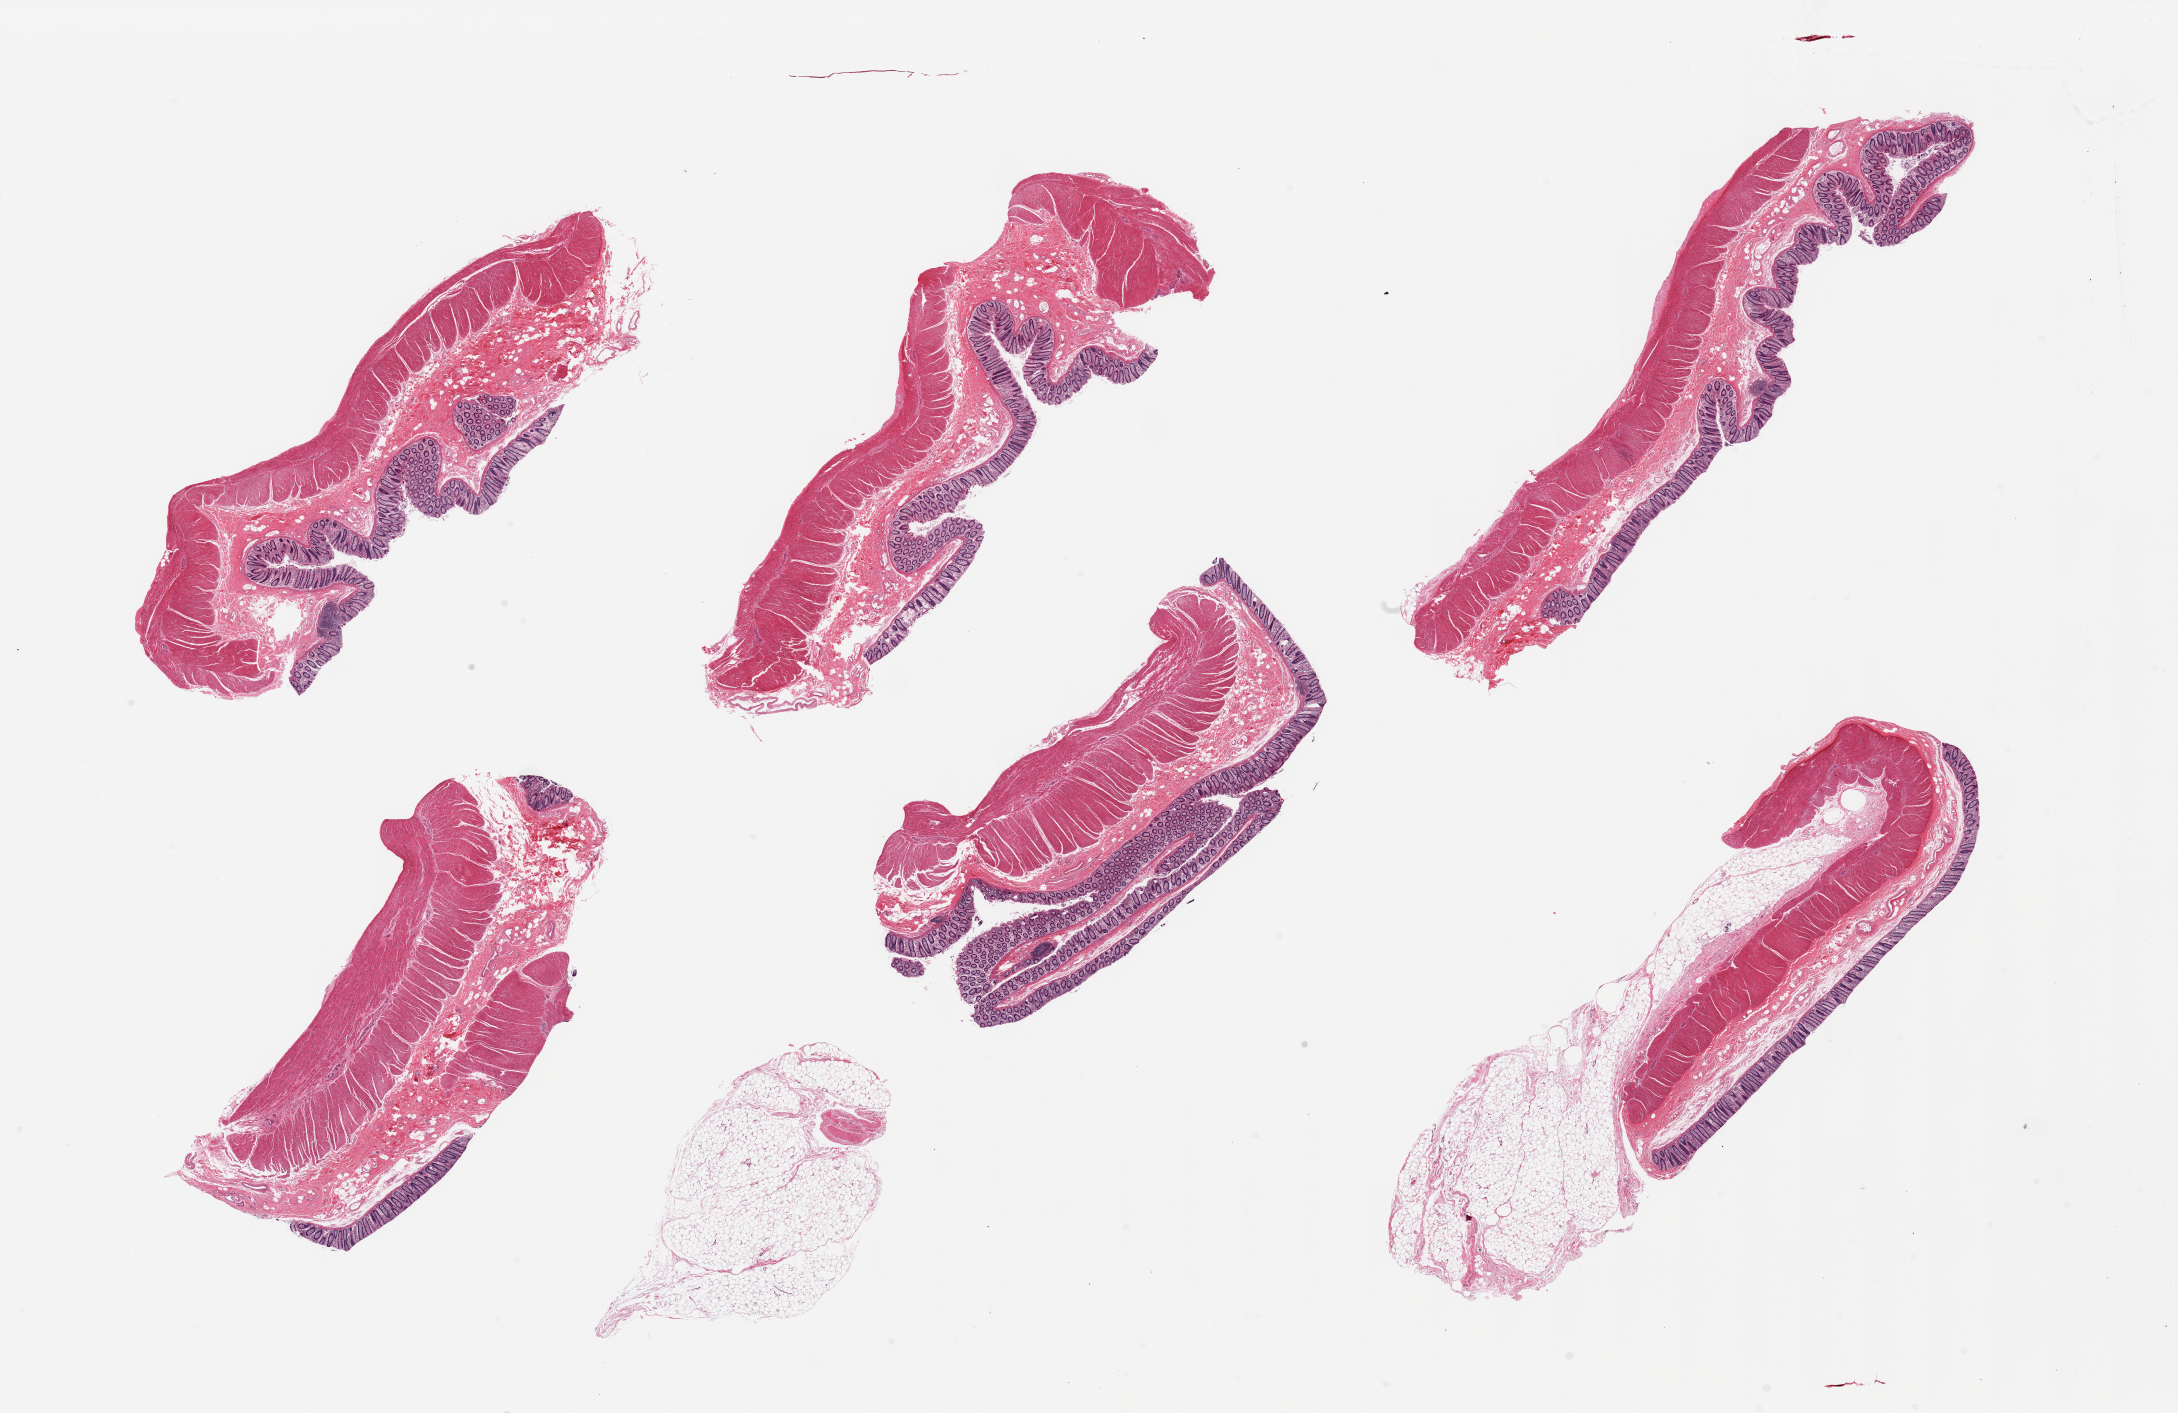
Digitized H&E-stained section, whole scanned area (about 34.5 x 22.4 mm, acquisition: 20x scan) shown as a low-resolution overview; PAXgene-fixed, paraffin-embedded tissue; section of transverse colon (target tissue); tissue donor sample.
Reviewer comment on this tissue sample: 6 pieces; well dissected except for 2 foci of external fat up to 3 mm thick.